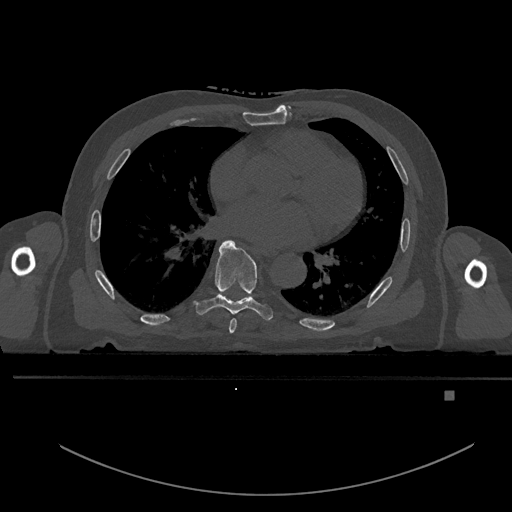
CT including the spine, one axial slice; slice 256 of 969 in the series (ordered by position); bone window (W 1800 / L 400 HU); 0.5 mm slice thickness; 512 × 512 image matrix, field of view 456 × 456 mm. Patient: male, 82 years. Case-level facts recorded for this patient, not image findings: primary cancer: prostate.
Outlined on this slice (semi-automatic segmentation, software-assisted and operator-edited):
- T6 vertebra: bounding box (x1, y1, x2, y2) in pixels: (229, 318, 237, 334)
- T7 vertebra: (193, 240, 273, 321)
- T8 vertebra: (226, 295, 254, 299)